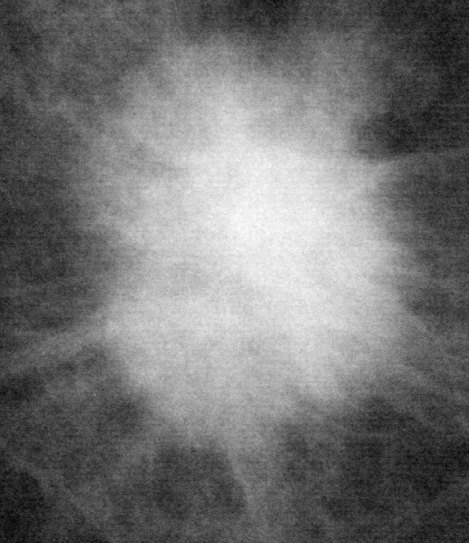
Crop from a digitized film mammogram around one marked abnormality; left breast; CC view.
Finding: mass, shape irregular, margins ill defined; BI-RADS assessment category 5; pathology result (as recorded, not read from the image): malignant.